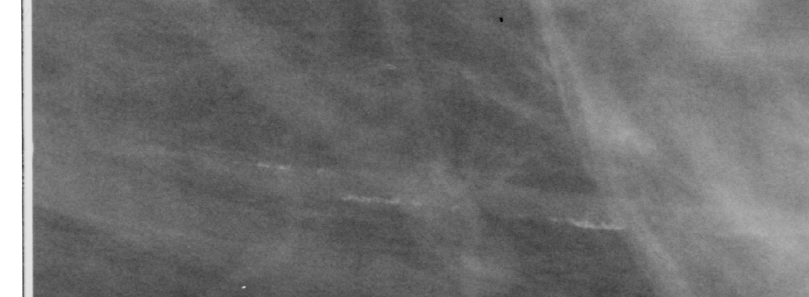
Crop from a digitized film mammogram around one marked abnormality, left breast, MLO view, BI-RADS breast density category 3 (scale 1–4).
Calcifications, morphology vascular / coarse; BI-RADS assessment category 2; subtlety rating 3 on a 1 (subtle) to 5 (obvious) scale; benign; no additional work-up was recommended (benign without callback).